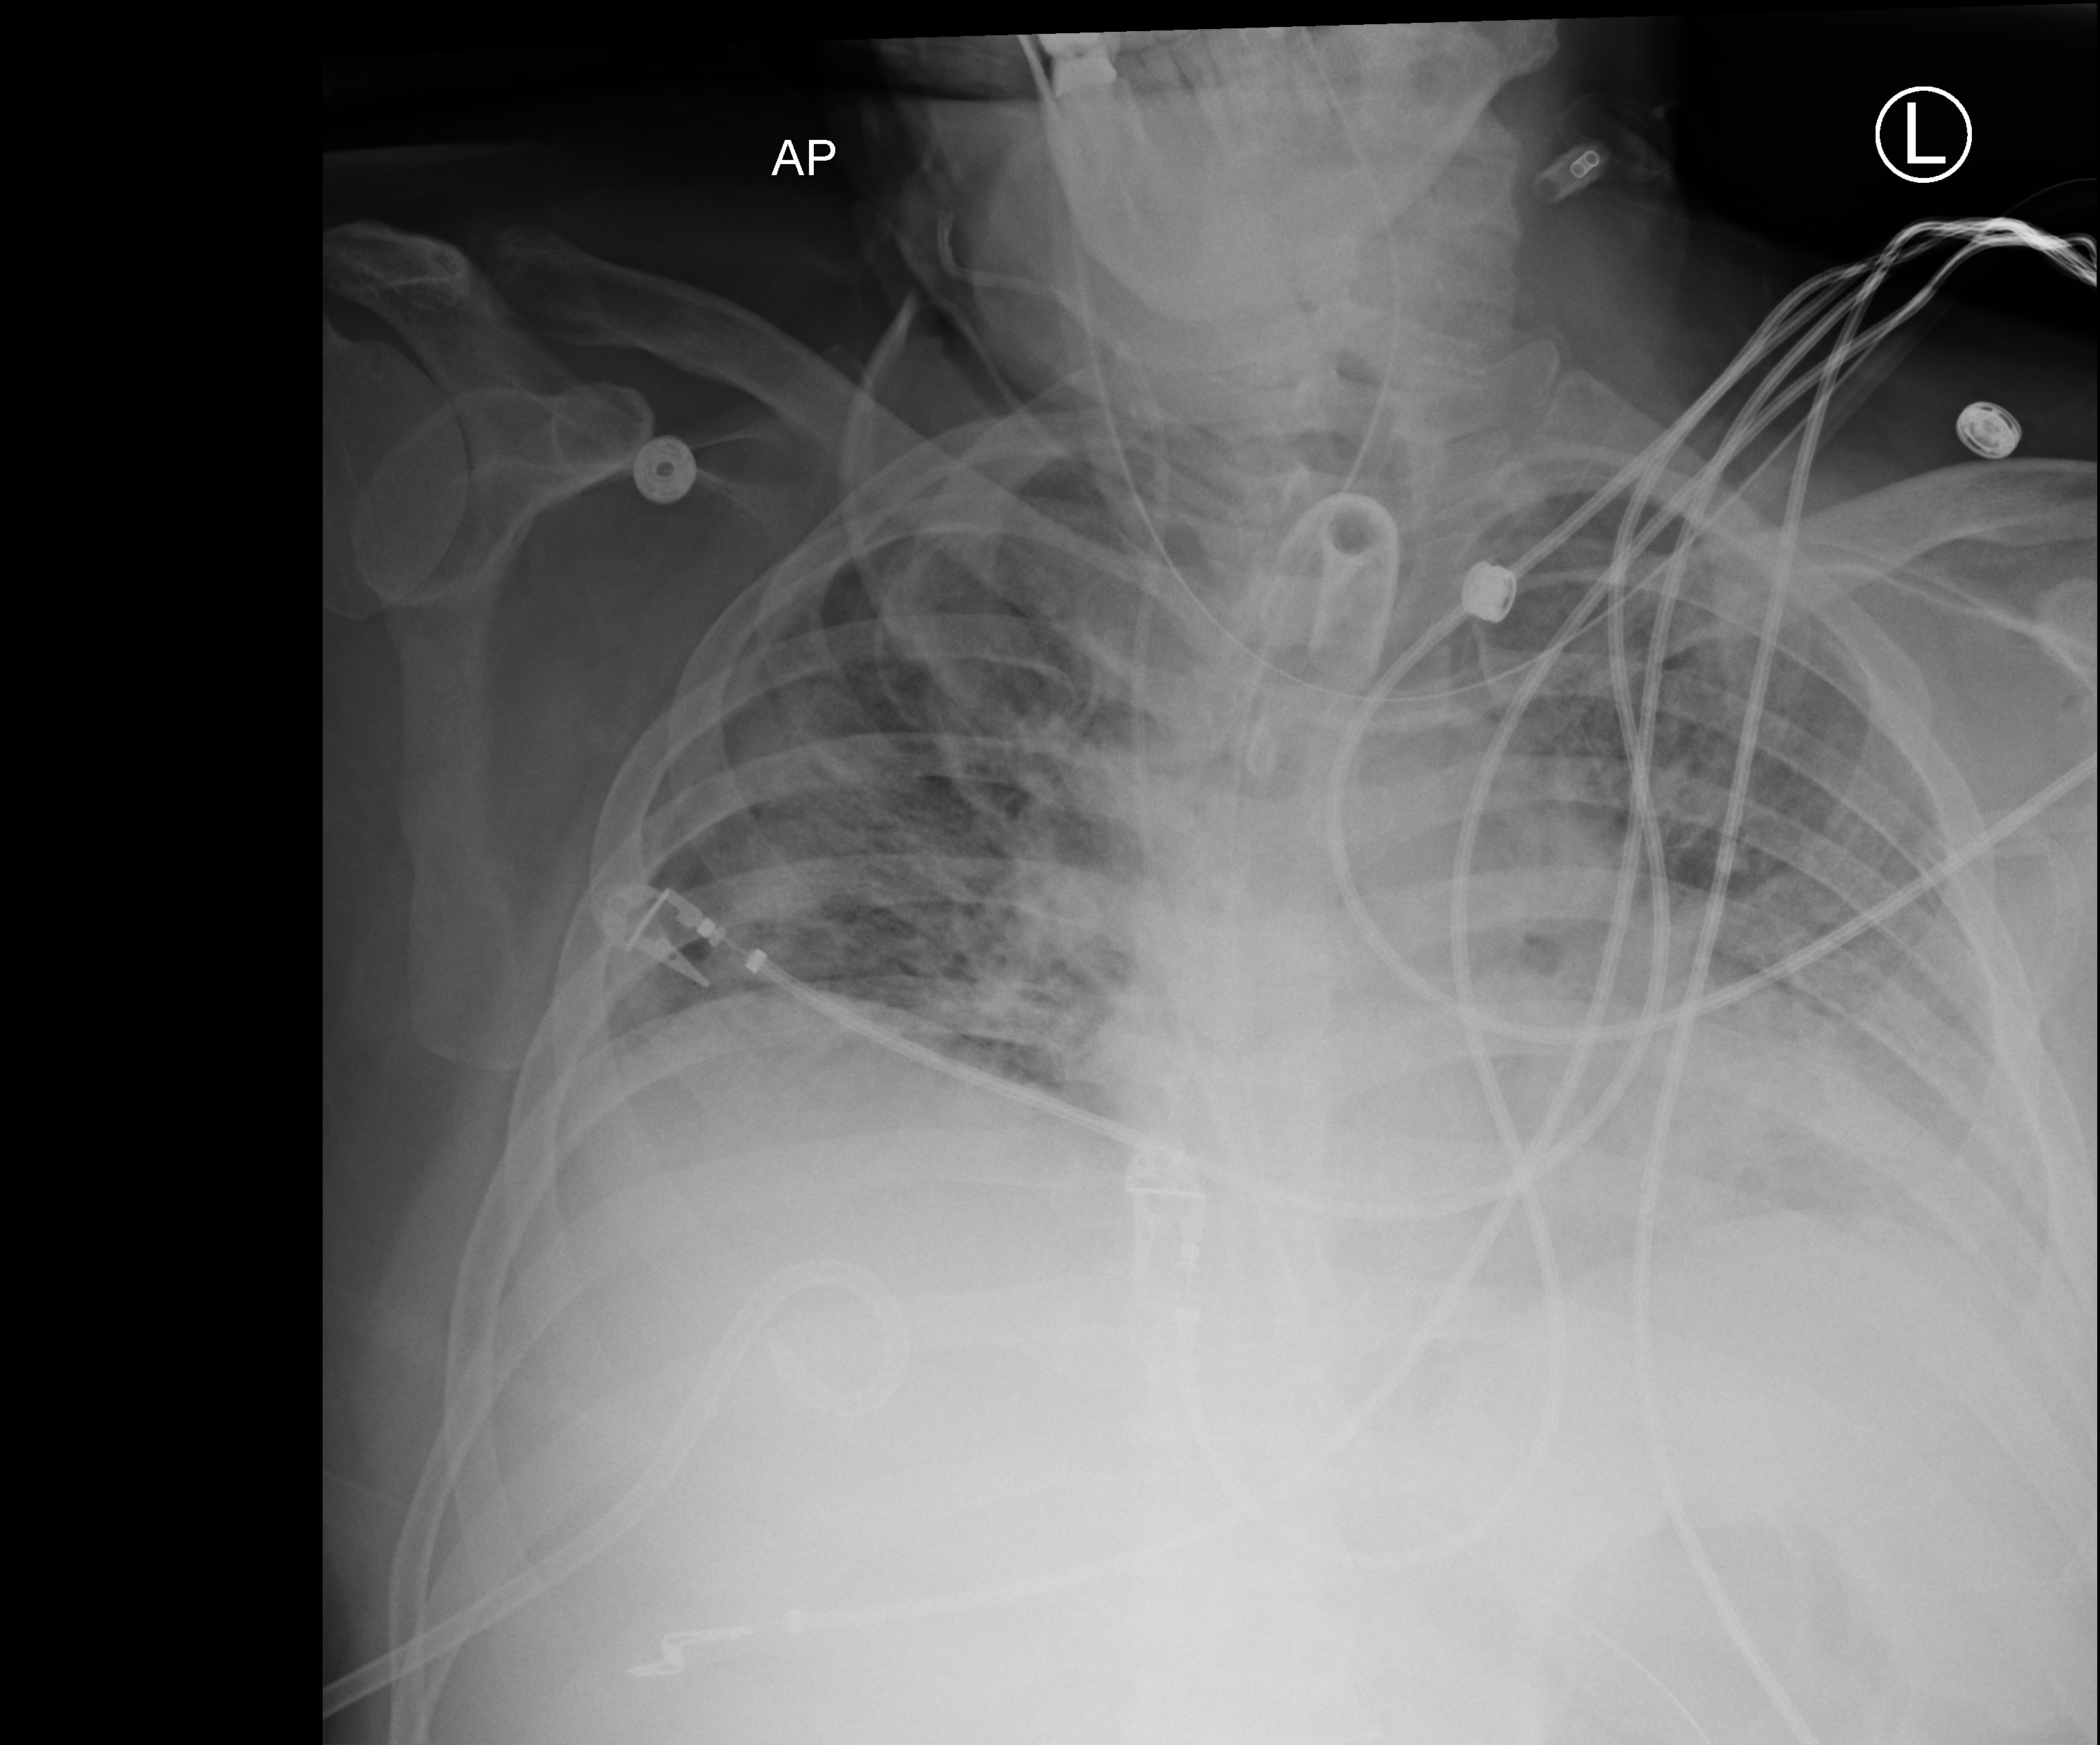
Chest X-ray (portable), anteroposterior (AP) projection. Male patient hospitalised with COVID-19, age 18–59 years.
From the hospital-stay record, not from the radiograph (when in the stay this image was taken is not recorded): length of hospital stay: 80 days.